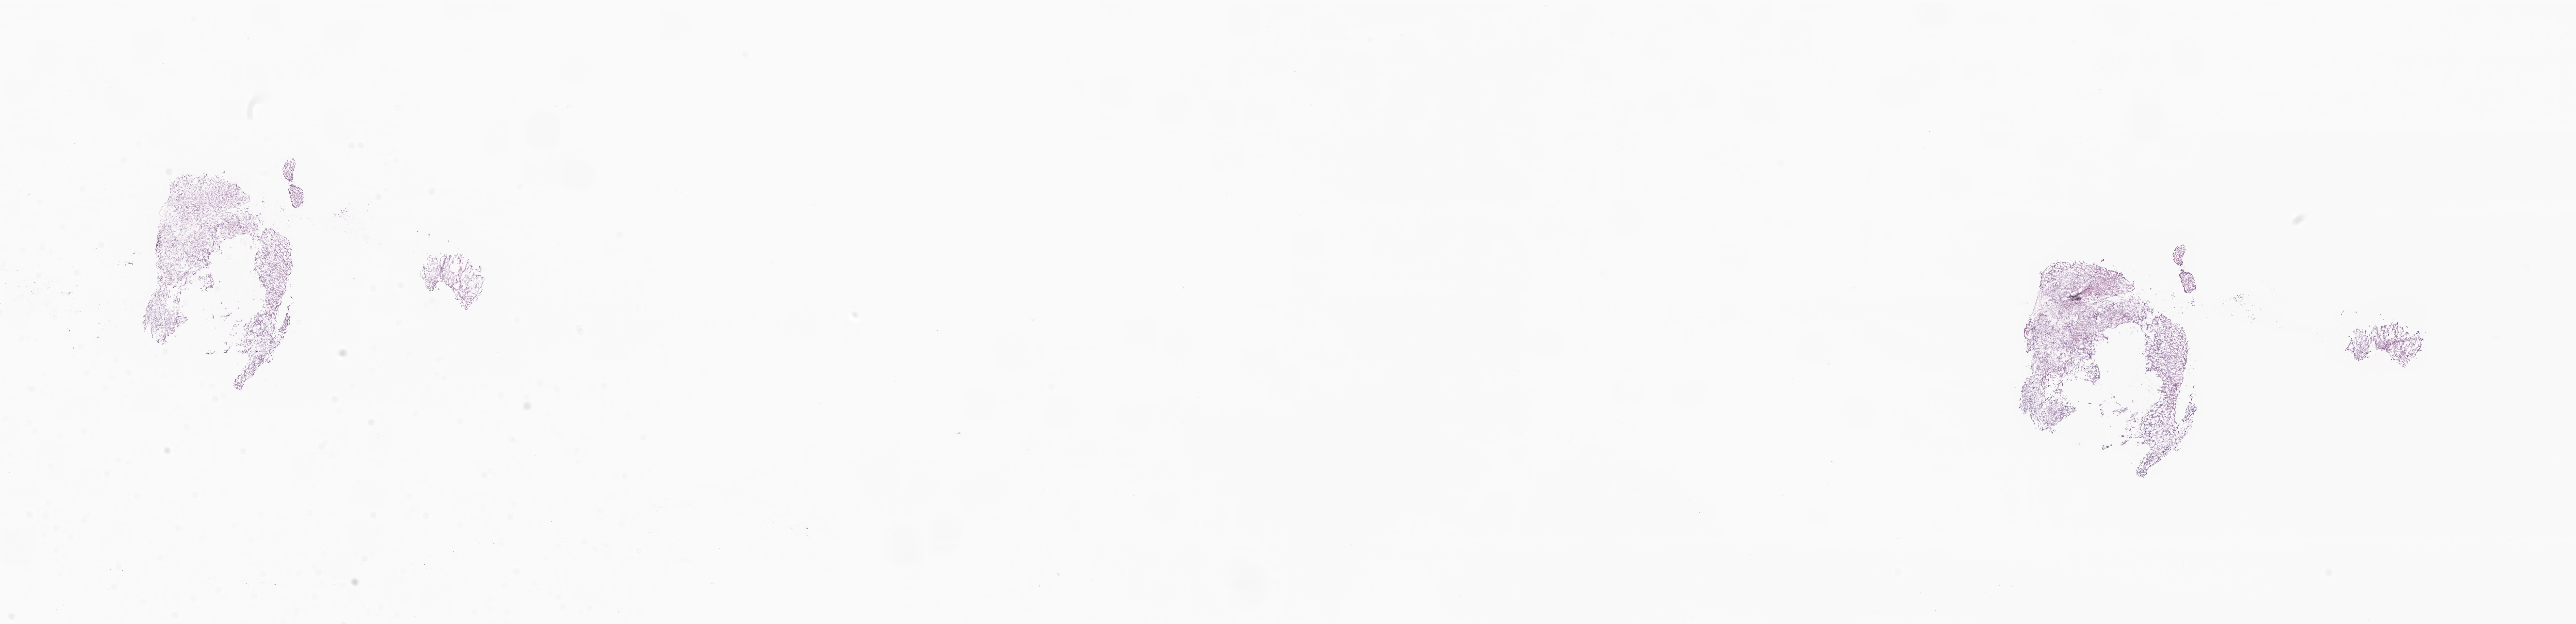
Haematoxylin and eosin whole-slide image of tumor tissue from the brain, a low-resolution overview of the entire scanned area, about 33.3 x 8.1 mm; frozen section (OCT-embedded). Patient female; age 48 months (4 years).
Recorded diagnosis: Glioma, malignant.